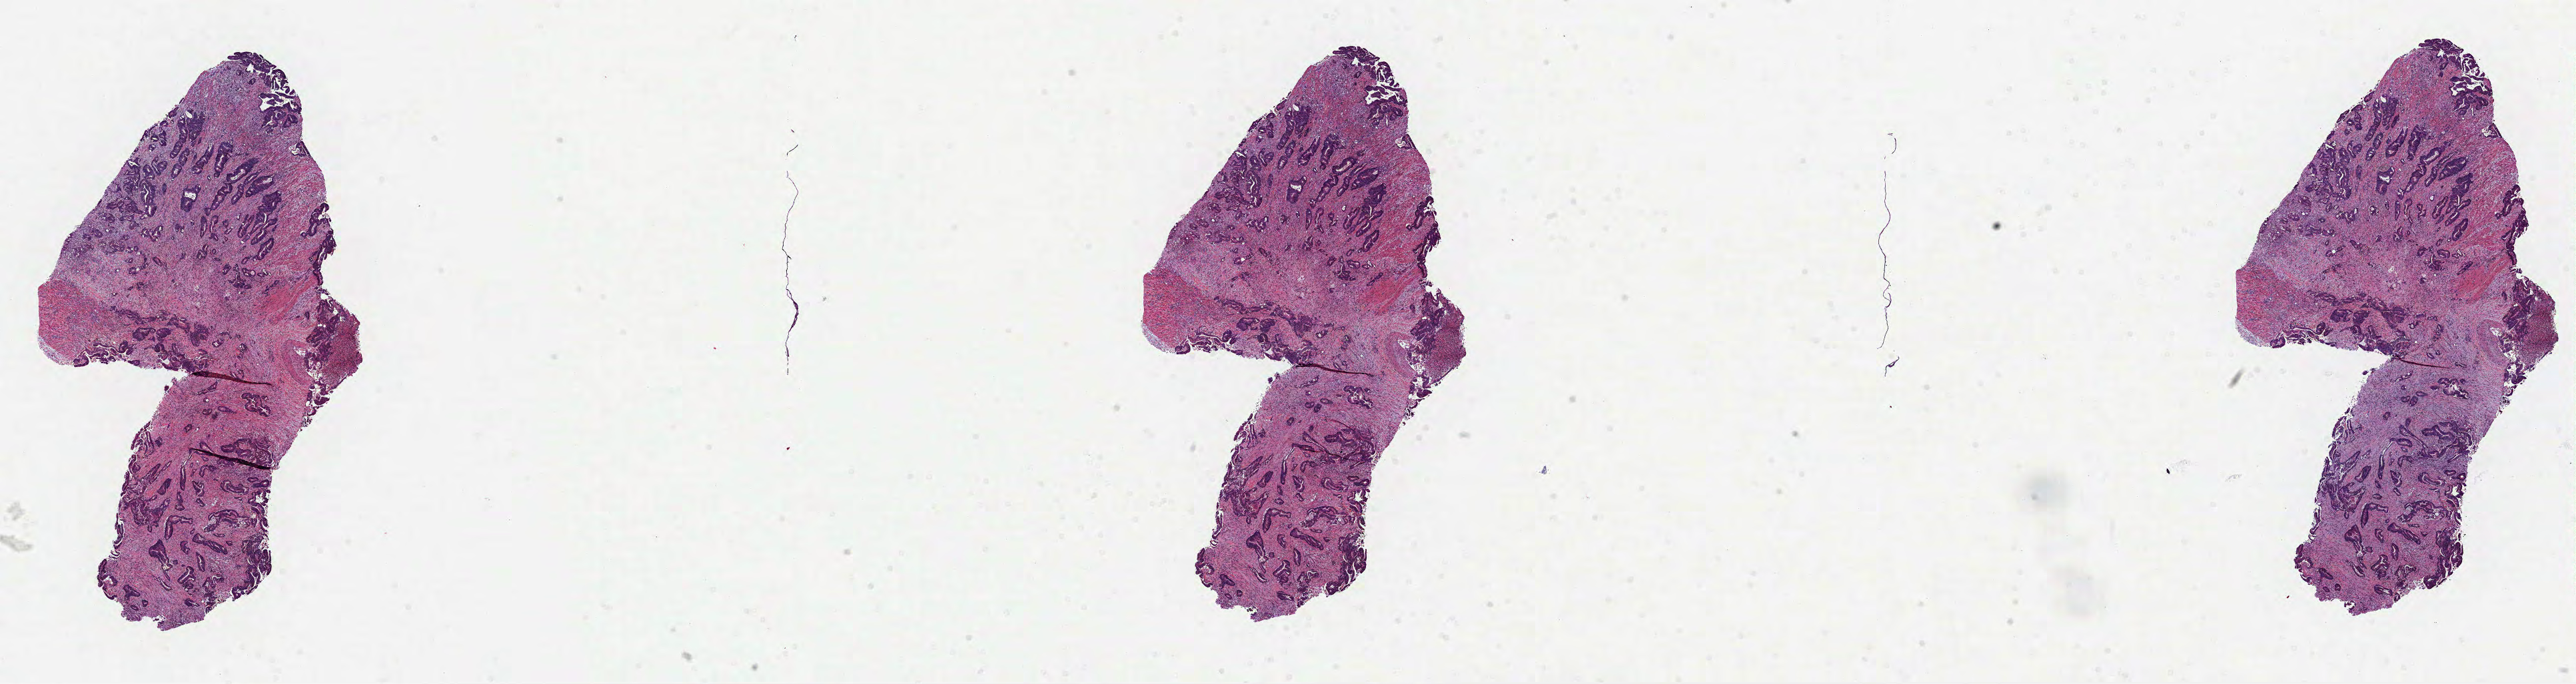
H&E whole-slide image — a low-resolution overview of the entire scanned area, about 31.2 x 8.3 mm (from a 40x scan), formalin-fixed paraffin-embedded (FFPE) diagnostic section, rectum, primary tumour sample. Male patient; age at initial diagnosis 60 years.
Diagnosis: Adenocarcinoma, NOS (rectosigmoid junction).